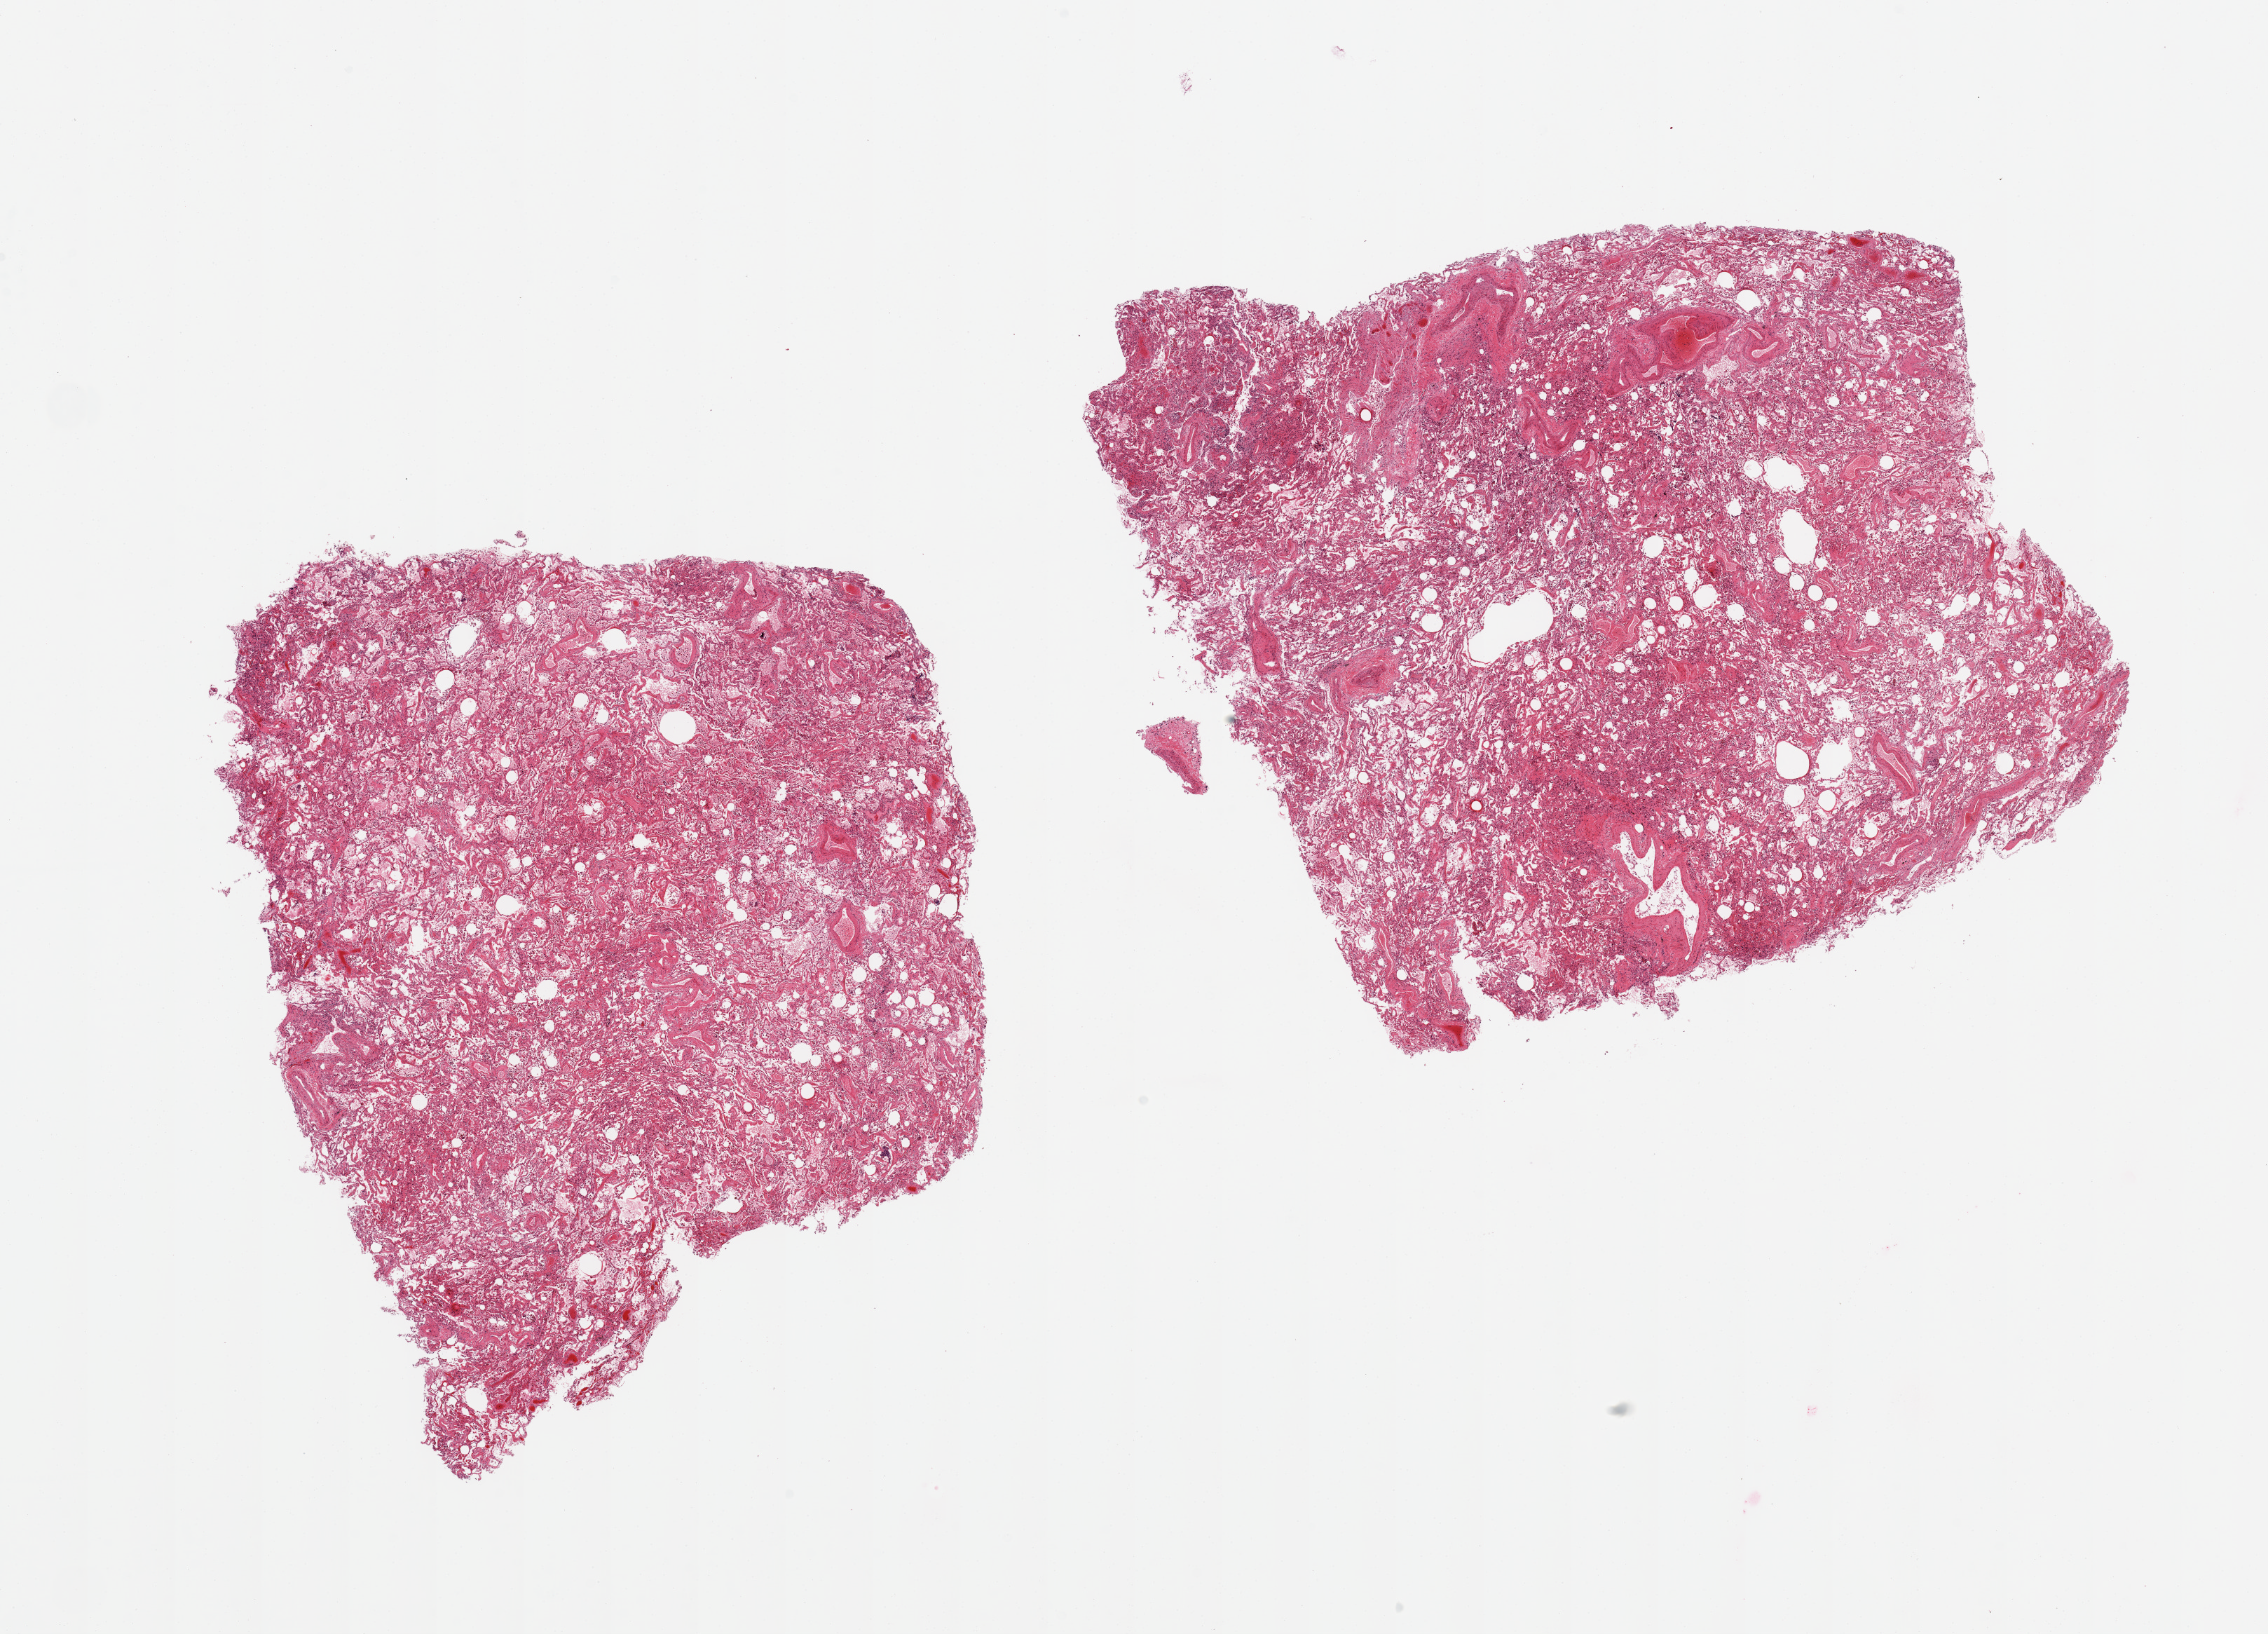
Whole-slide image, H&E stain — whole scanned area (about 25.6 x 18.4 mm, acquisition: 20x scan) shown as a low-resolution overview. PAXgene-fixed paraffin-embedded (PFPE) section. Sampled site (target tissue): lung. Tissue donor sample. Male donor.
• pathologist's review note for this sample: 2 pieces; congestion, fibrosis, pigmented macrophages